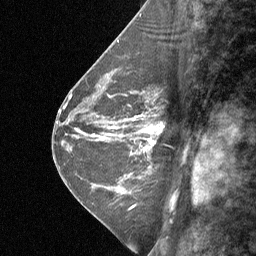
Breast MRI (dynamic contrast-enhanced), one sagittal slice; slice 28 of 64 in the series (ordered by position); dynamic contrast-enhanced study with each time point stored as its own series, time point 2 of 3 at this slice position (early post-contrast, ordered by acquisition time); 1.5 T; TE 4.8 ms, TR 27 ms; 256 × 256 image matrix, field of view 180 × 180 mm. Female patient, age 42 years. Case-level facts recorded for this patient, not image findings: setting: breast cancer imaged before/during neoadjuvant chemotherapy; receptor status: triple-negative.
Annotated regions visible in this slice (semi-automatic segmentation, software-assisted and operator-edited):
- analysis volume of interest (the breast-tissue region the enhancement analysis was run in; not a lesion): bounding box (x1, y1, x2, y2) in pixels: (124, 94, 177, 161)
- tumour enhancement mask (voxels above the 90 % enhancement threshold inside the analysis volume of interest): (144, 128, 162, 145)